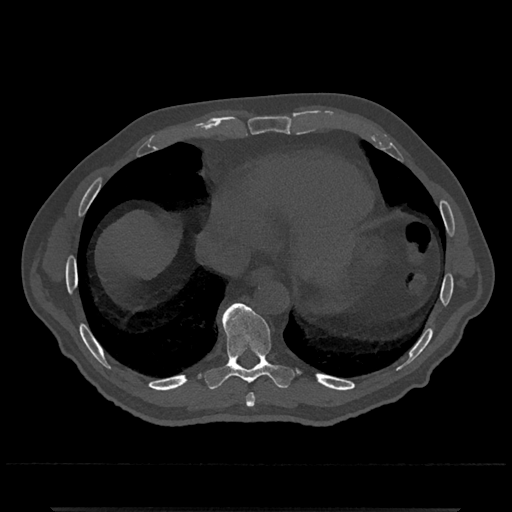
CT including the spine, one axial slice; reconstruction kernel Br40s/3; bone window (W 1800 / L 400 HU); 0.5 mm slice thickness; 512 × 512 image matrix, field of view 393 × 393 mm. Male patient, age 67 years. From the clinical record (not read from this slice): primary cancer: prostate.
Structures marked on this image (semi-automatic segmentation, software-assisted and operator-edited):
- T8 vertebra: bounding box (x1, y1, x2, y2) in pixels: (246, 393, 255, 407)
- T9 vertebra: (204, 303, 295, 390)